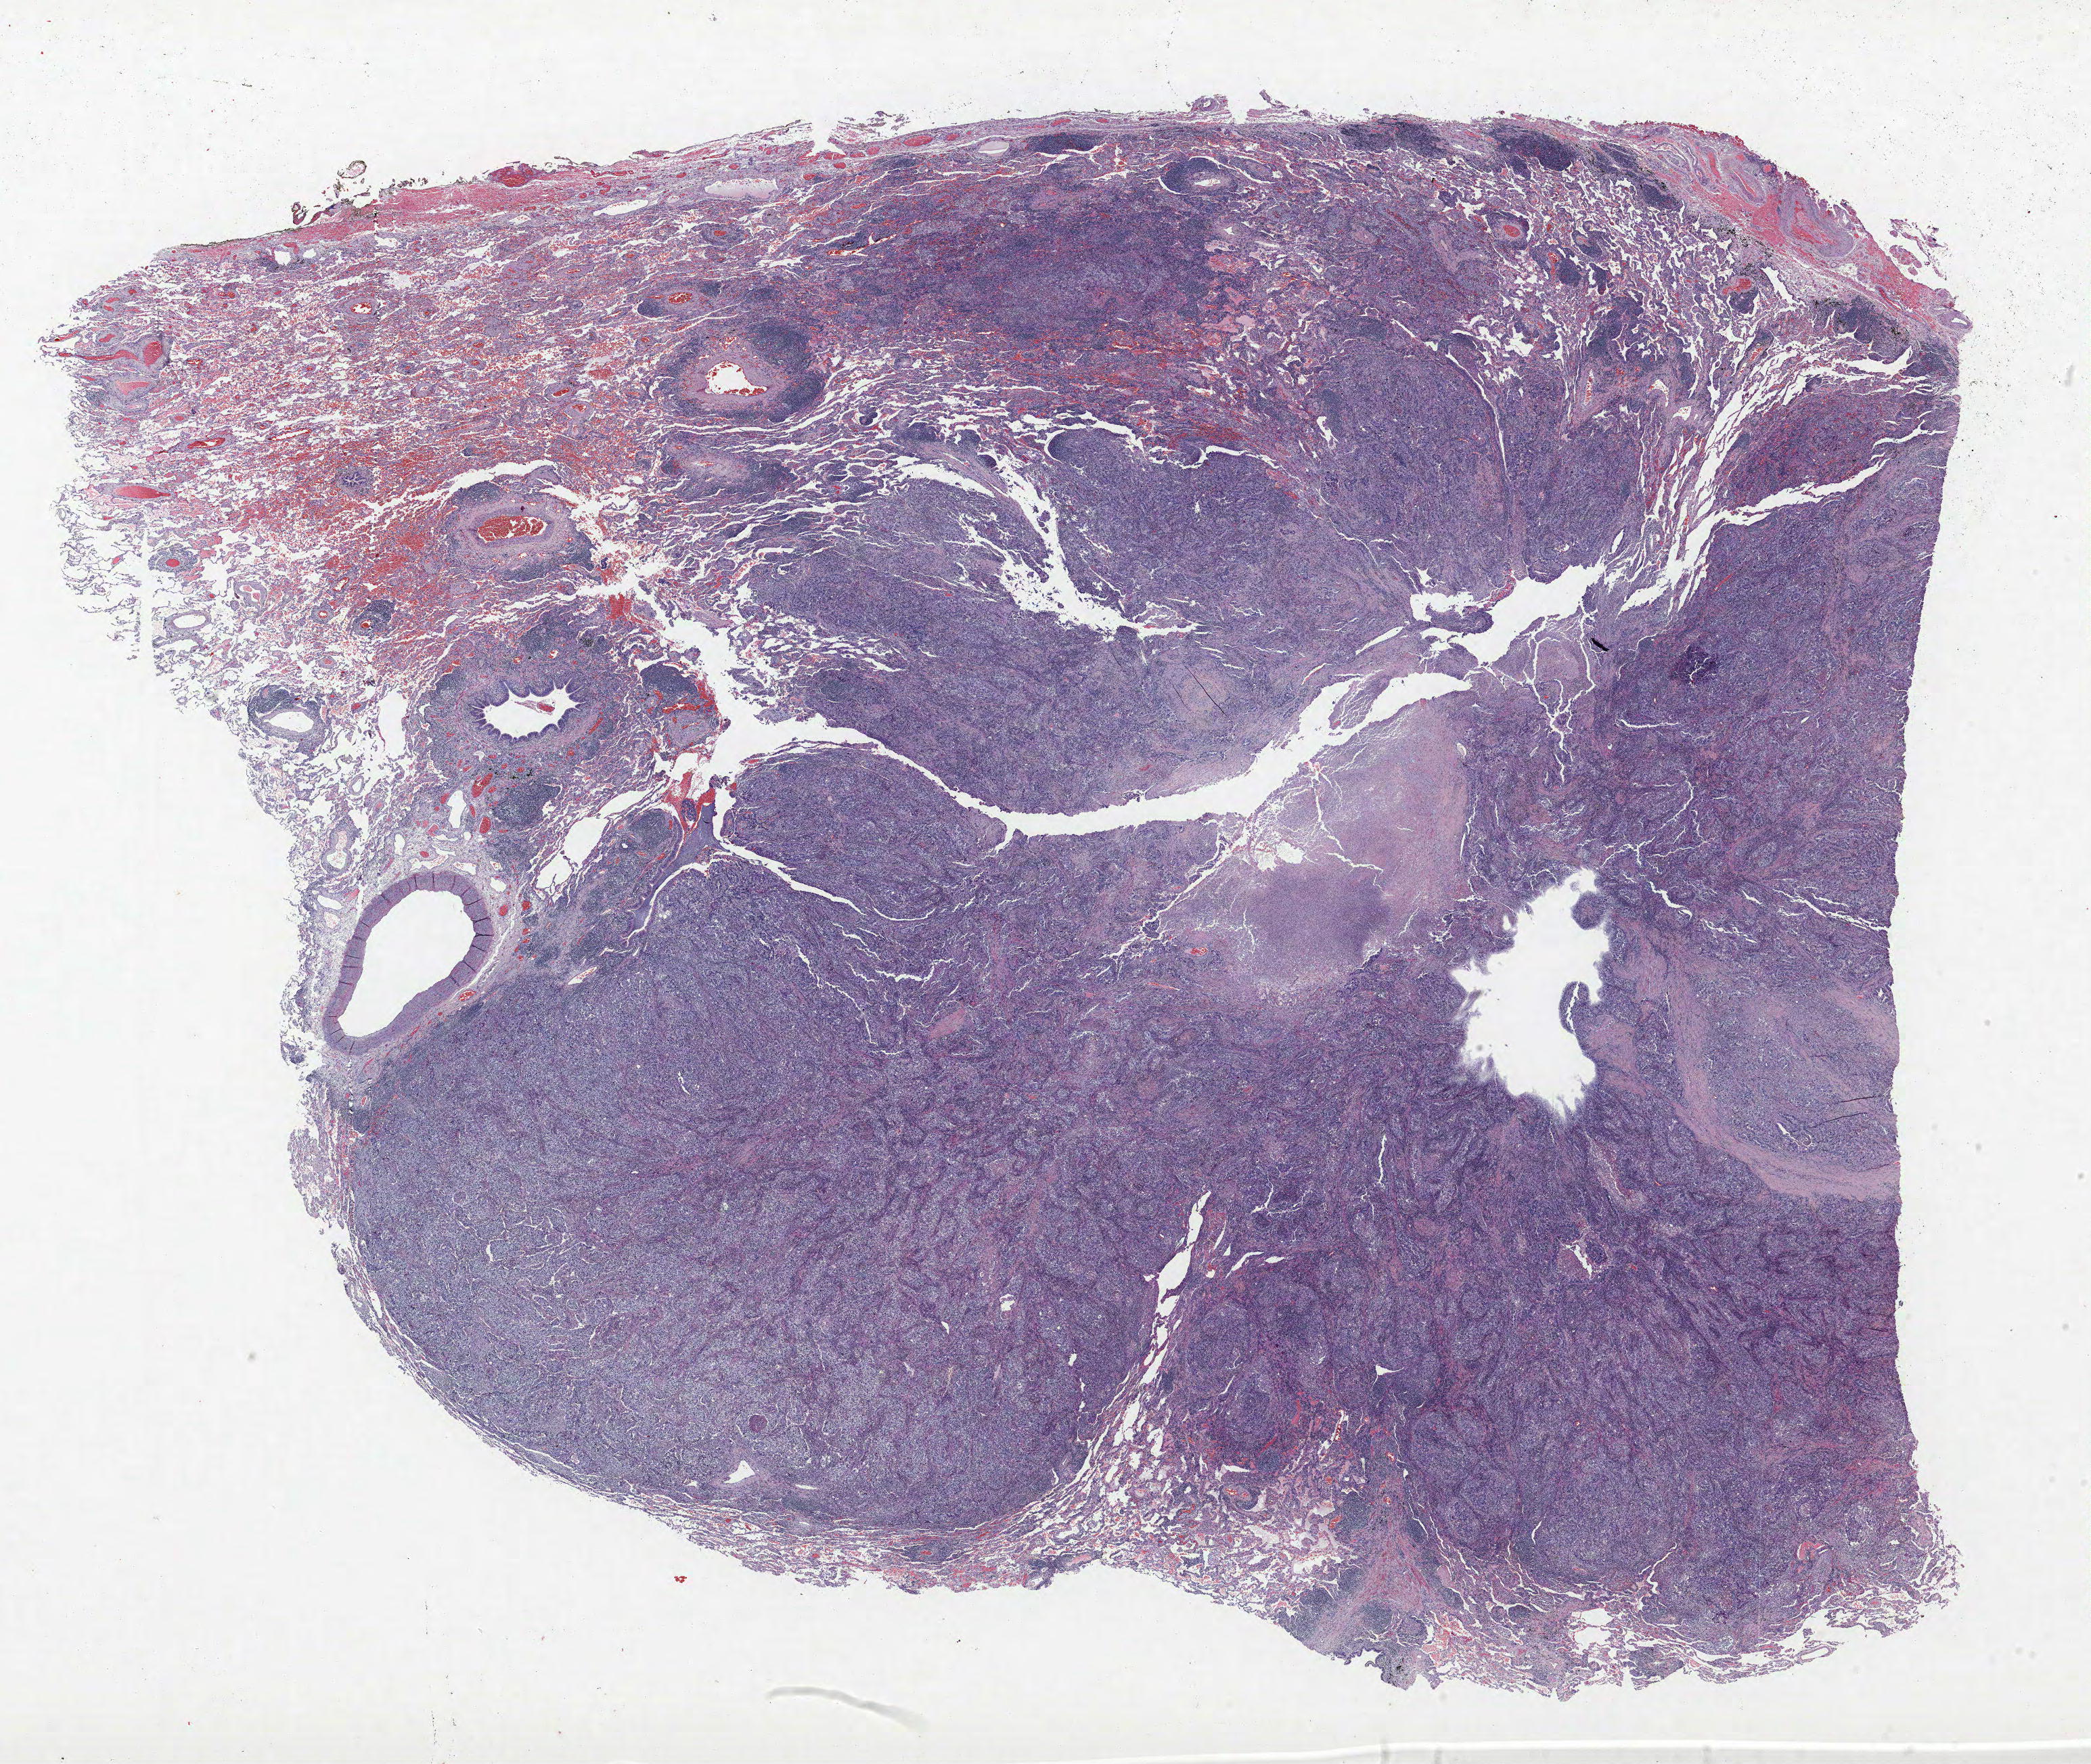
H&E-stained whole-slide image — whole scanned area (about 24.7 x 20.9 mm) shown as a low-resolution overview; FFPE section; lung tissue. Male patient, aged 73 at enrolment. Current smoker at enrolment. Grade: poorly differentiated (G3).
Primary tumour location (clinical record): right upper lobe. Stage (AJCC 6th edition): IA. Participant's lung-cancer diagnosis: Adenocarcinoma, NOS. Tumour size (pathology): 22 mm.